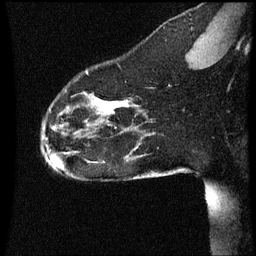
Breast MRI (dynamic contrast-enhanced), one sagittal slice; position 15 of 60 along the scan axis; dynamic contrast-enhanced series, image 2 of 3 at this slice position (ordered by acquisition); 1.5 T; TE 4.2 ms, TR 8.9 ms; 256 × 256 image matrix, field of view 200 × 200 mm. Female patient, age 35 years. From the clinical record (not read from this slice): setting: breast cancer imaged before/during neoadjuvant chemotherapy; receptor status: HER2-positive.
Annotated regions visible in this slice (semi-automatic segmentation, software-assisted and operator-edited):
- analysis volume of interest (the breast-tissue region the enhancement analysis was run in; not a lesion): box from (x=40, y=66) to (x=177, y=177) px
- tumour enhancement mask (voxels above the 70 % enhancement threshold inside the analysis volume of interest): (x=98, y=100)–(x=129, y=111)